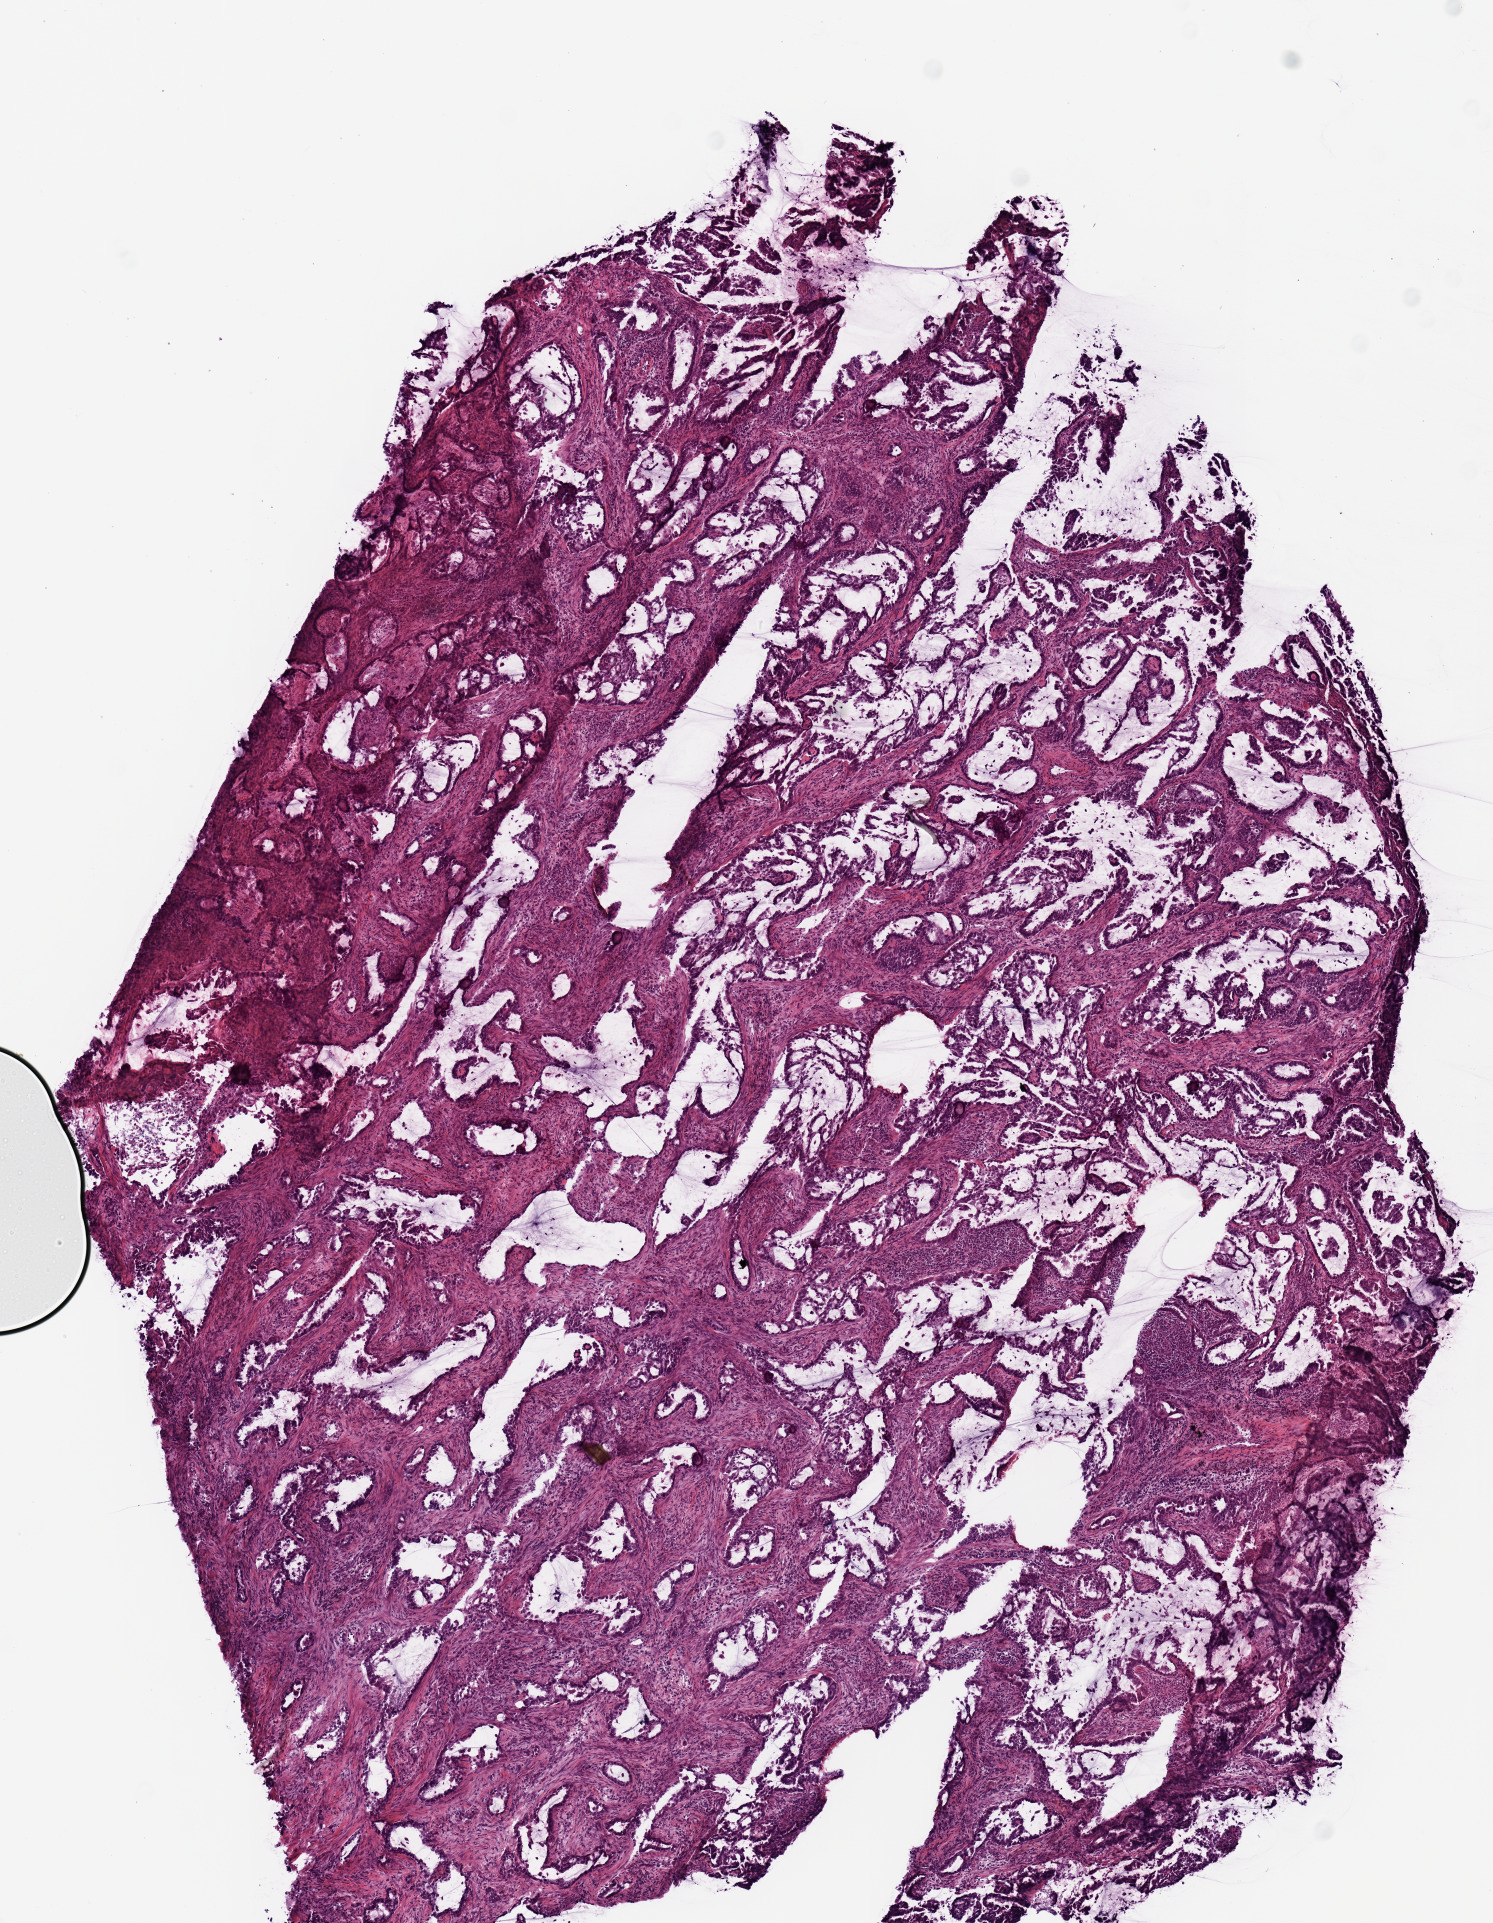
Digitized H&E tissue section (whole slide) — shown as a low-resolution overview of the whole scanned area (about 5.9 x 7.6 mm). Frozen section from the top of the tissue portion. Sample: primary tumour, lung. Female patient; age at initial diagnosis 77 years. Slide review estimates, as recorded: tumour cells 80%, tumour nuclei 60%, normal cells 0%, stromal cells 20%, necrosis 0%.
- laterality: left
- AJCC pathologic stage: IA (6th edition)
- histologic diagnosis: Adenocarcinoma with mixed subtypes (lower lobe, lung)